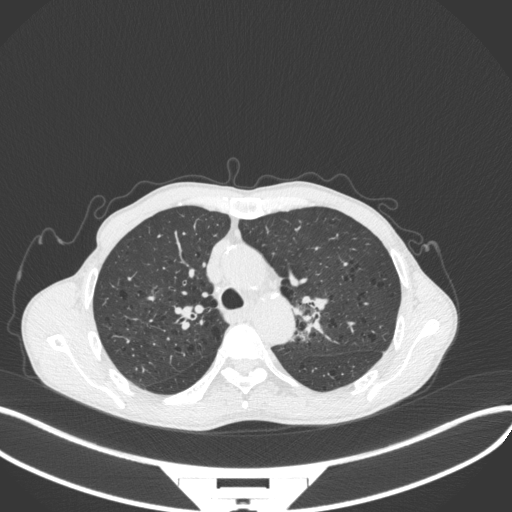
Chest CT, one axial slice. Position 301 of 394 along the scan axis. 120 kVp. Lung window (W 1500 / L -600 HU). 512 × 512 image matrix, field of view 400 × 400 mm. Patient: male, 65 years. Case-level facts recorded for this patient, not image findings: clinical TNM (as recorded): T2b N0 M0.
Structures marked on this image (rectangle marked by the reading radiologist):
- lung tumour (recorded histology: adenocarcinoma): bounding box [x1, y1, x2, y2] px = [292, 291, 330, 348]